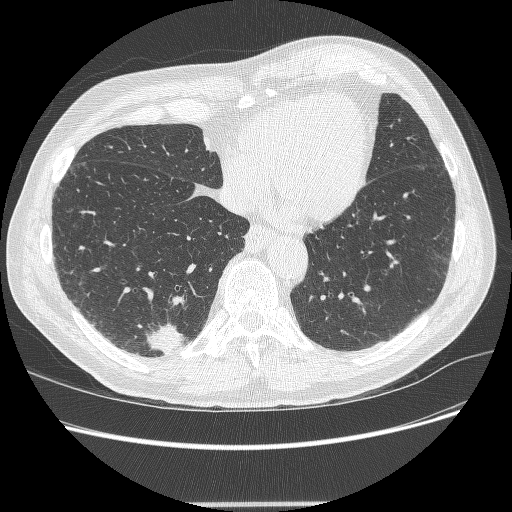
Low-dose screening chest CT, axial slice; second screening round (one year after baseline); lung window (W 1500 / L -600 HU); 1.25 mm slice thickness; lung (sharp) reconstruction kernel (BONE); slice 71 of 245 in the series; 512 × 512 image matrix, field of view 372 × 372 mm. Male, age 71 years at enrolment.
Expert-annotated lung lesion, bounding box (x1, y1, x2, y2) in pixels: (137, 322, 189, 362). The screening reader recorded 5 non-calcified nodules or masses ≥4 mm on this exam; which of them this box marks is not recorded. Official screen result: positive, change unspecified: nodule(s) >= 4 mm or enlarging nodule(s), mass(es), or other non-specific abnormalities suspicious for lung cancer. Lung cancer was diagnosed 7 days after this screen: squamous cell carcinoma, NOS, right lower lobe, moderately differentiated (G2), stage IA (AJCC 6th edition), 27 mm at pathology.